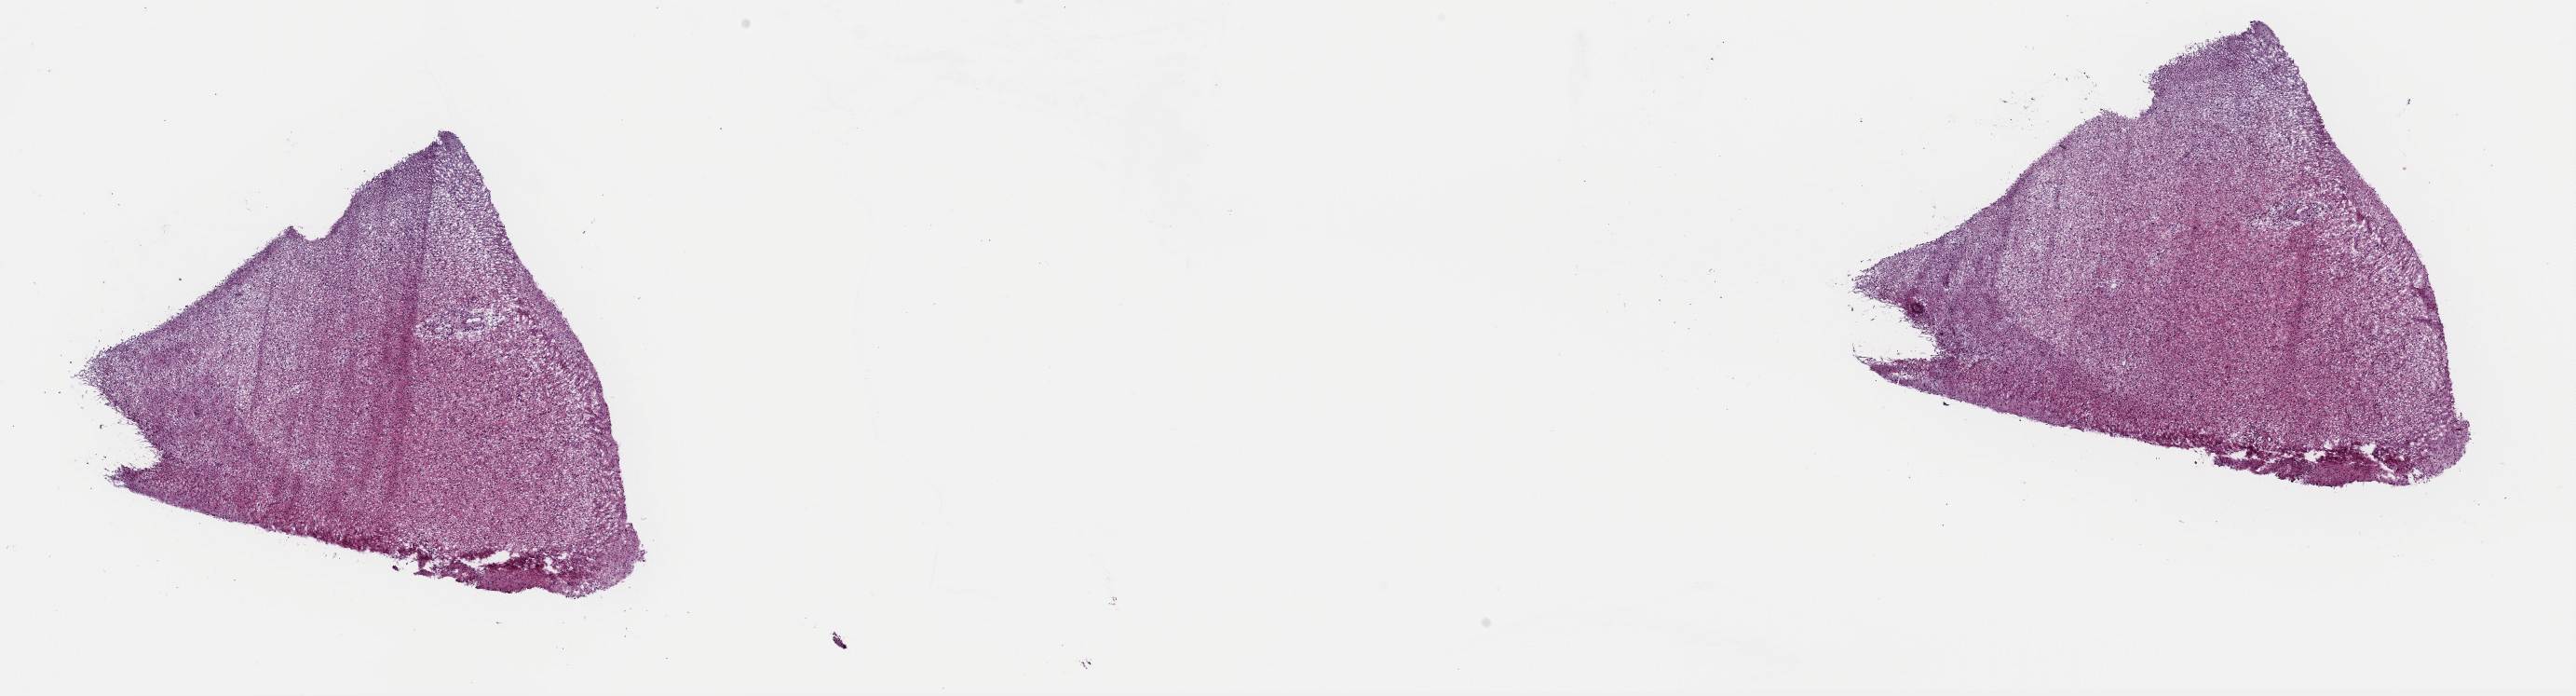
Whole-slide histology image, Hematoxylin and eosin (H&E) stained, whole scanned area (about 21.9 x 5.9 mm, acquisition: 40x scan) shown as a low-resolution overview; frozen section from the top of the tissue portion; brain, primary tumour sample. Patient: male, age at initial diagnosis 33 years. Histologic grade: G3 (poorly differentiated). Composition of this section per pathologist review: tumour cells 90%, tumour nuclei 90%, normal cells 5%, stromal cells 5%, necrosis 0%. Inflammatory infiltration, as recorded: lymphocyte infiltration 0%, monocyte infiltration 0%, neutrophil infiltration 0%.
• pathologic diagnosis: Astrocytoma, anaplastic